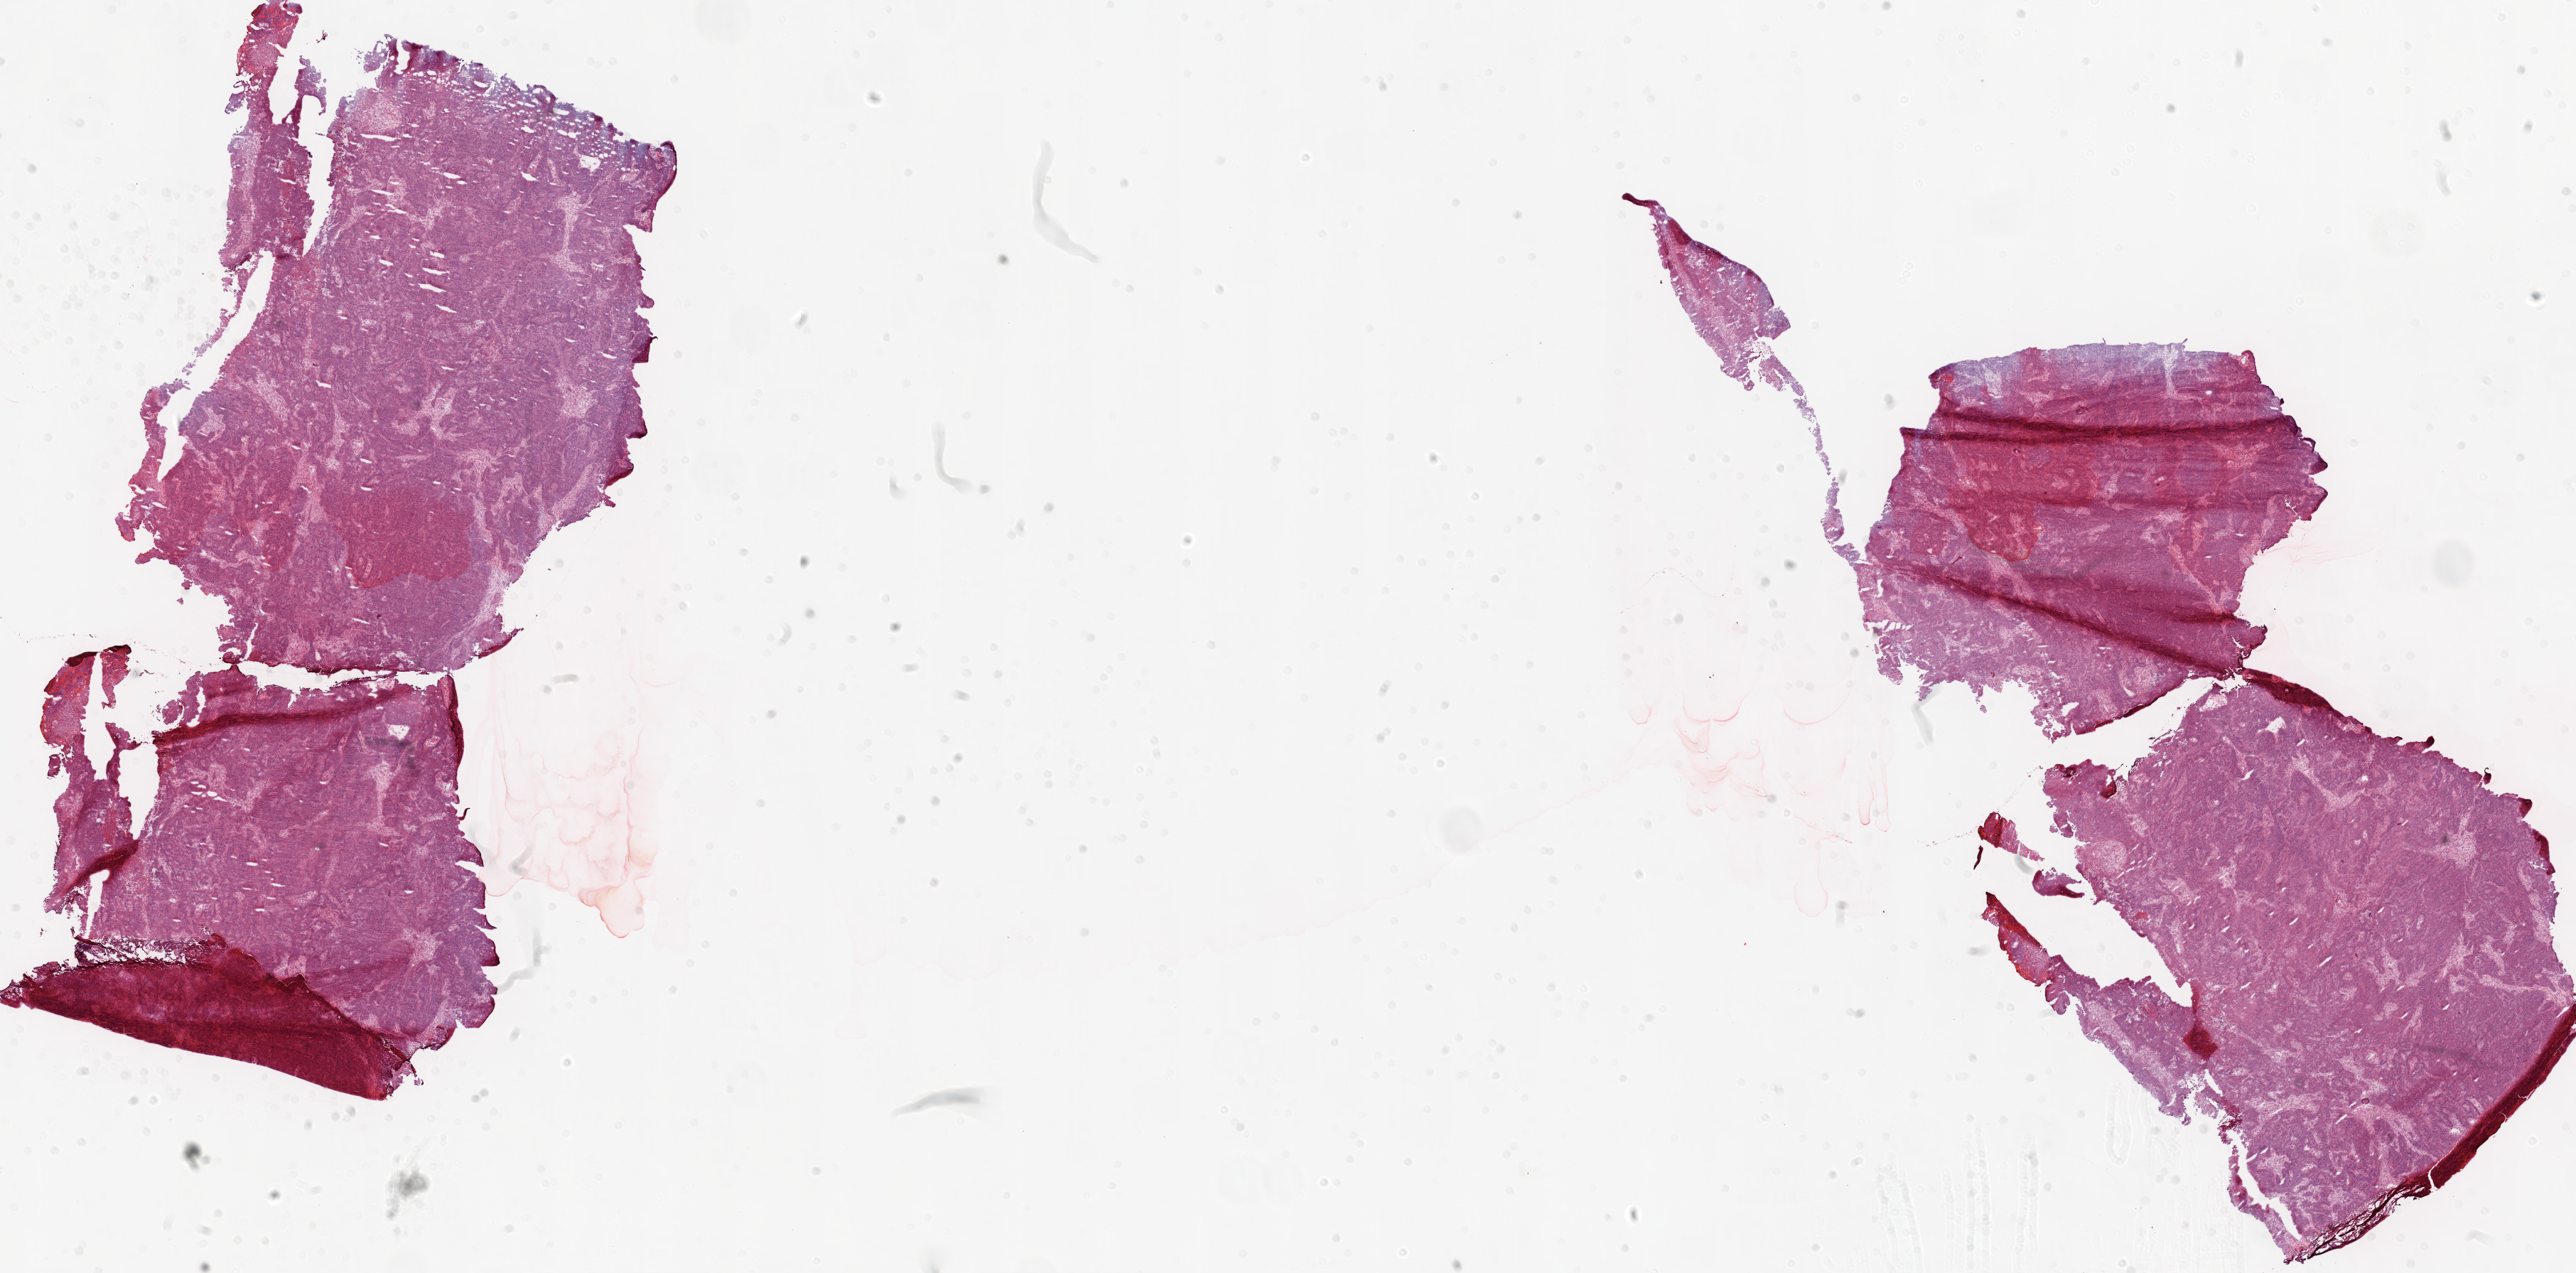
Digitized H&E-stained tissue section (whole slide) — shown as a low-resolution overview of the whole scanned area (about 29.1 x 14.4 mm, from a 20x scan). Frozen section from the top of the tissue portion. Sample: primary tumour, ovary. Female patient; age at initial diagnosis 52 years. Histologic grade: G3 (poorly differentiated). Pathologist review of this section (percent, as recorded): tumour cells 90%, tumour nuclei 95%, normal cells 0%, stromal cells 8%, necrosis 2%. Infiltration values recorded for this section: lymphocyte infiltration 1%.
• FIGO stage: IIIC
• diagnosis: Serous cystadenocarcinoma, NOS